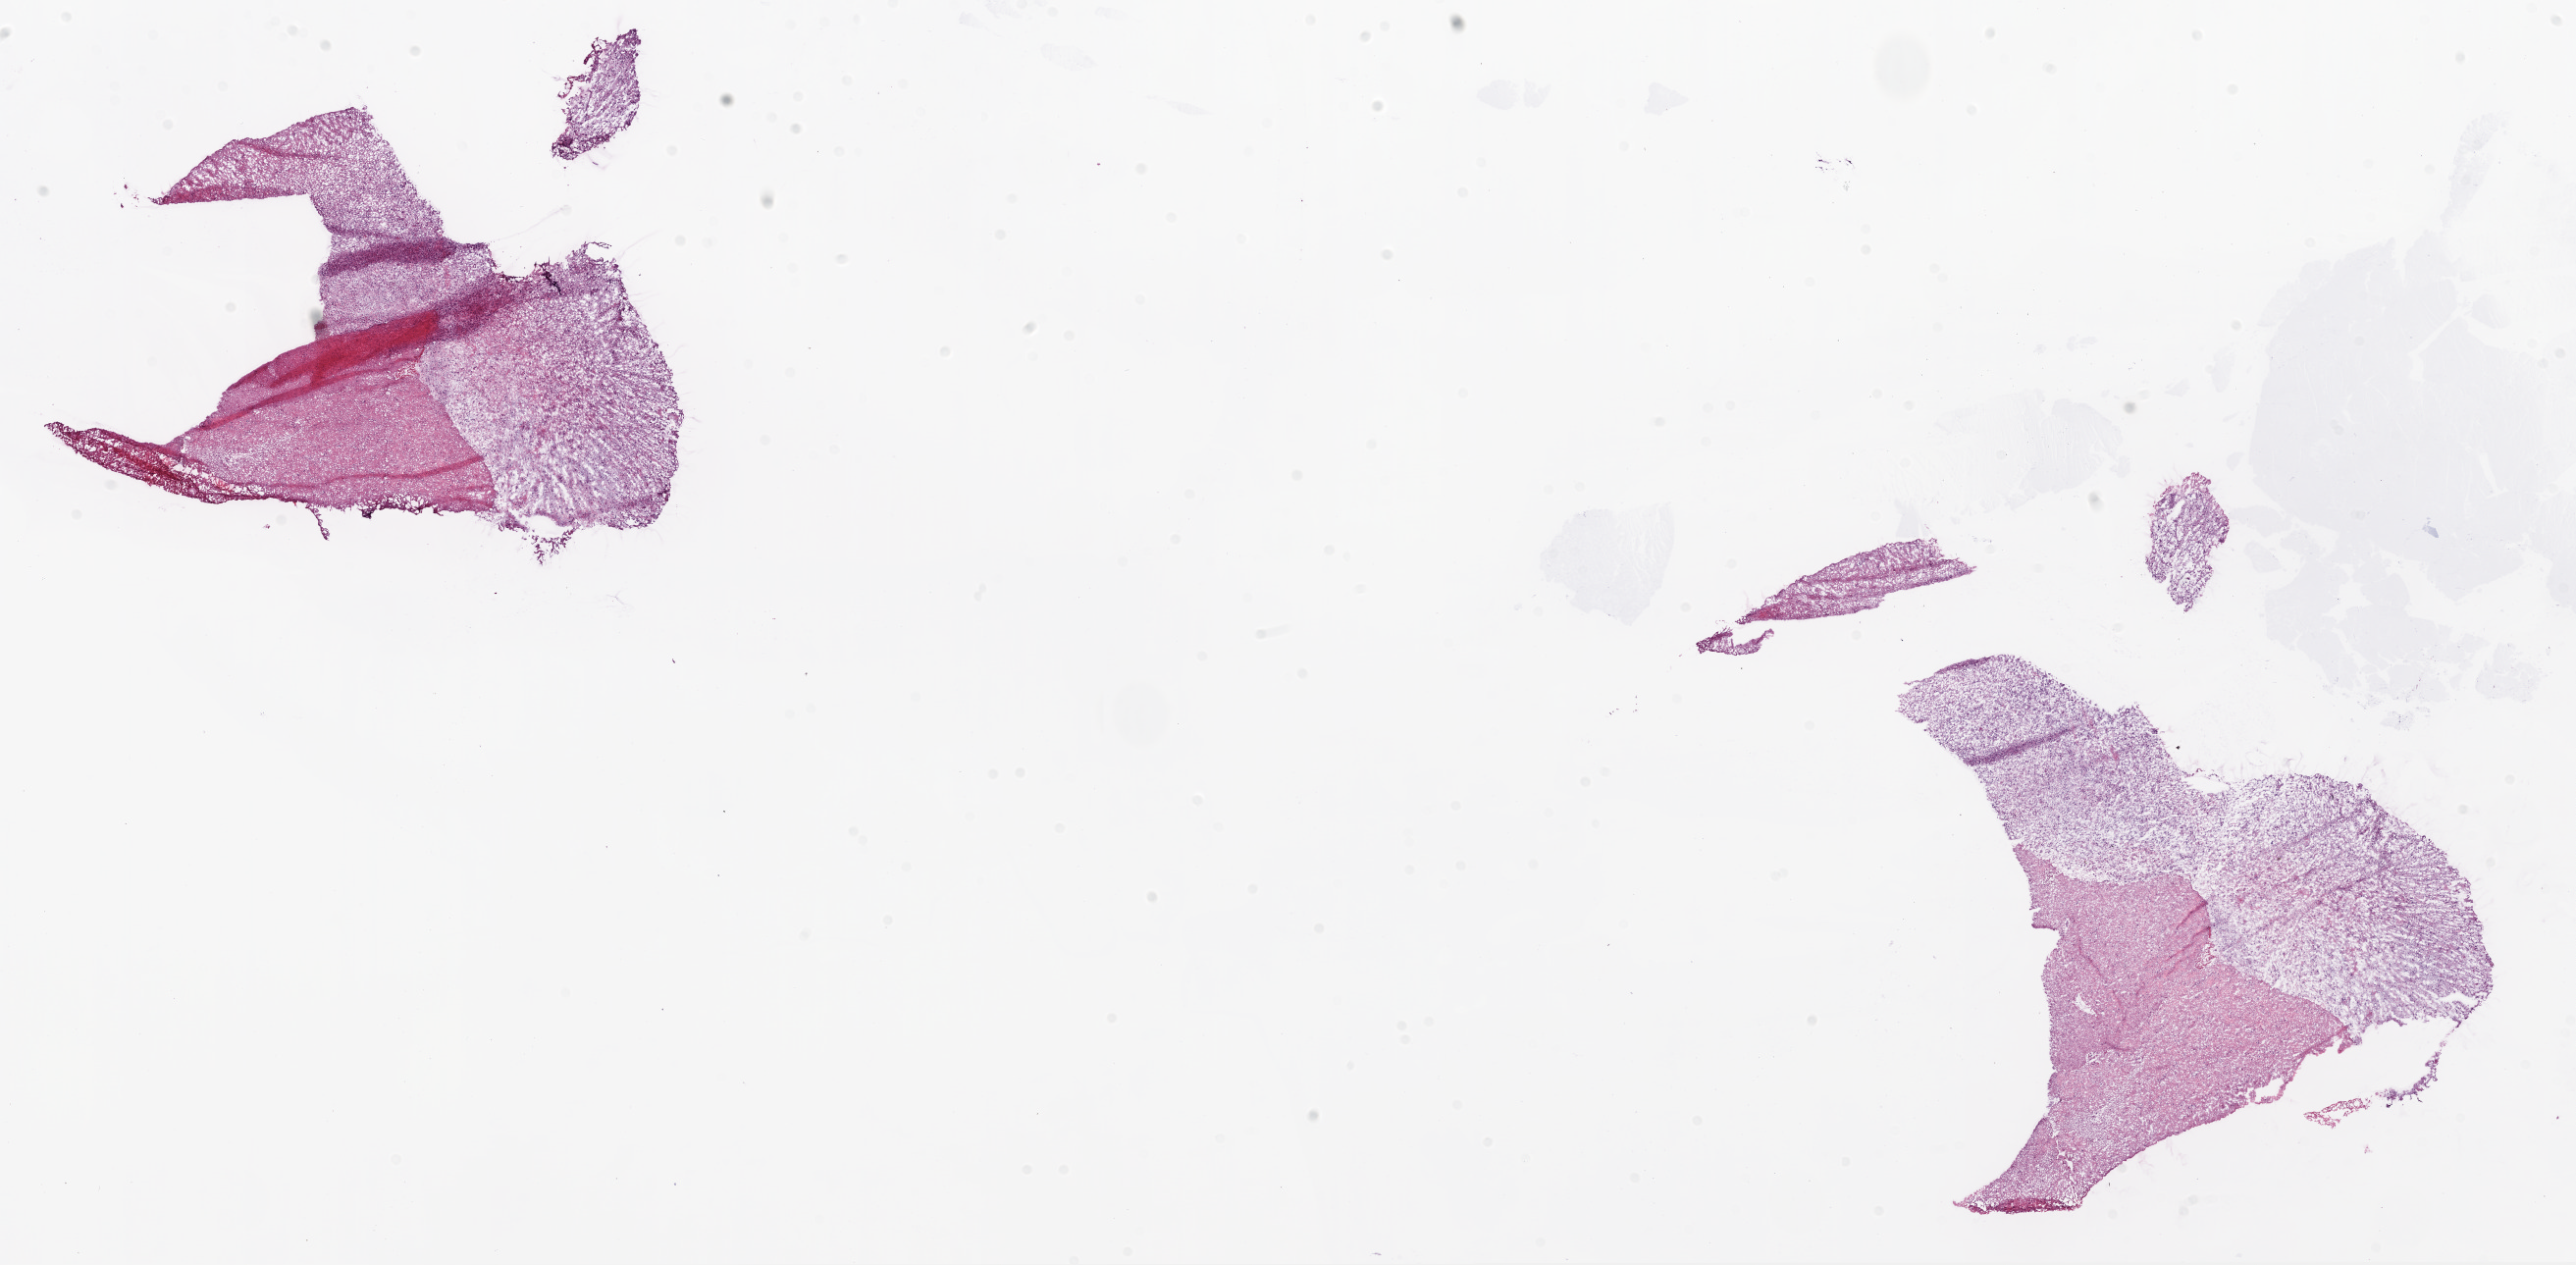
H&E whole-slide image — whole scanned area (about 21.1 x 10.3 mm) shown as a low-resolution overview. Frozen section. Sample: primary tumour, brain. Patient: male, age at initial diagnosis 65 years. Pathologist review of this section (percent, as recorded): tumour cells 100%, tumour nuclei 80%, normal cells 0%, stromal cells 0%, necrosis 0%.
Histologic diagnosis: Glioblastoma.